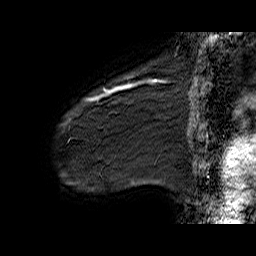
Breast MRI (dynamic contrast-enhanced), one sagittal slice; slice 9 of 60 in the series (ordered by position); dynamic contrast-enhanced series, time point 2 of 6 at this slice position (early post-contrast); 1.5 T; TE 6.4 ms, TR 32.9 ms; 256 × 256 image matrix. Female patient. Case-level facts recorded for this patient, not image findings: setting: breast cancer imaged before/during neoadjuvant chemotherapy; receptor status: HER2-positive.
Structures marked on this image (semi-automatic segmentation, software-assisted and operator-edited):
- analysis volume of interest (the breast-tissue region the enhancement analysis was run in; not a lesion): bounding box [x1, y1, x2, y2] px = [61, 77, 141, 142]
- tumour enhancement mask (voxels above the 100 % enhancement threshold inside the analysis volume of interest): [85, 82, 141, 101]